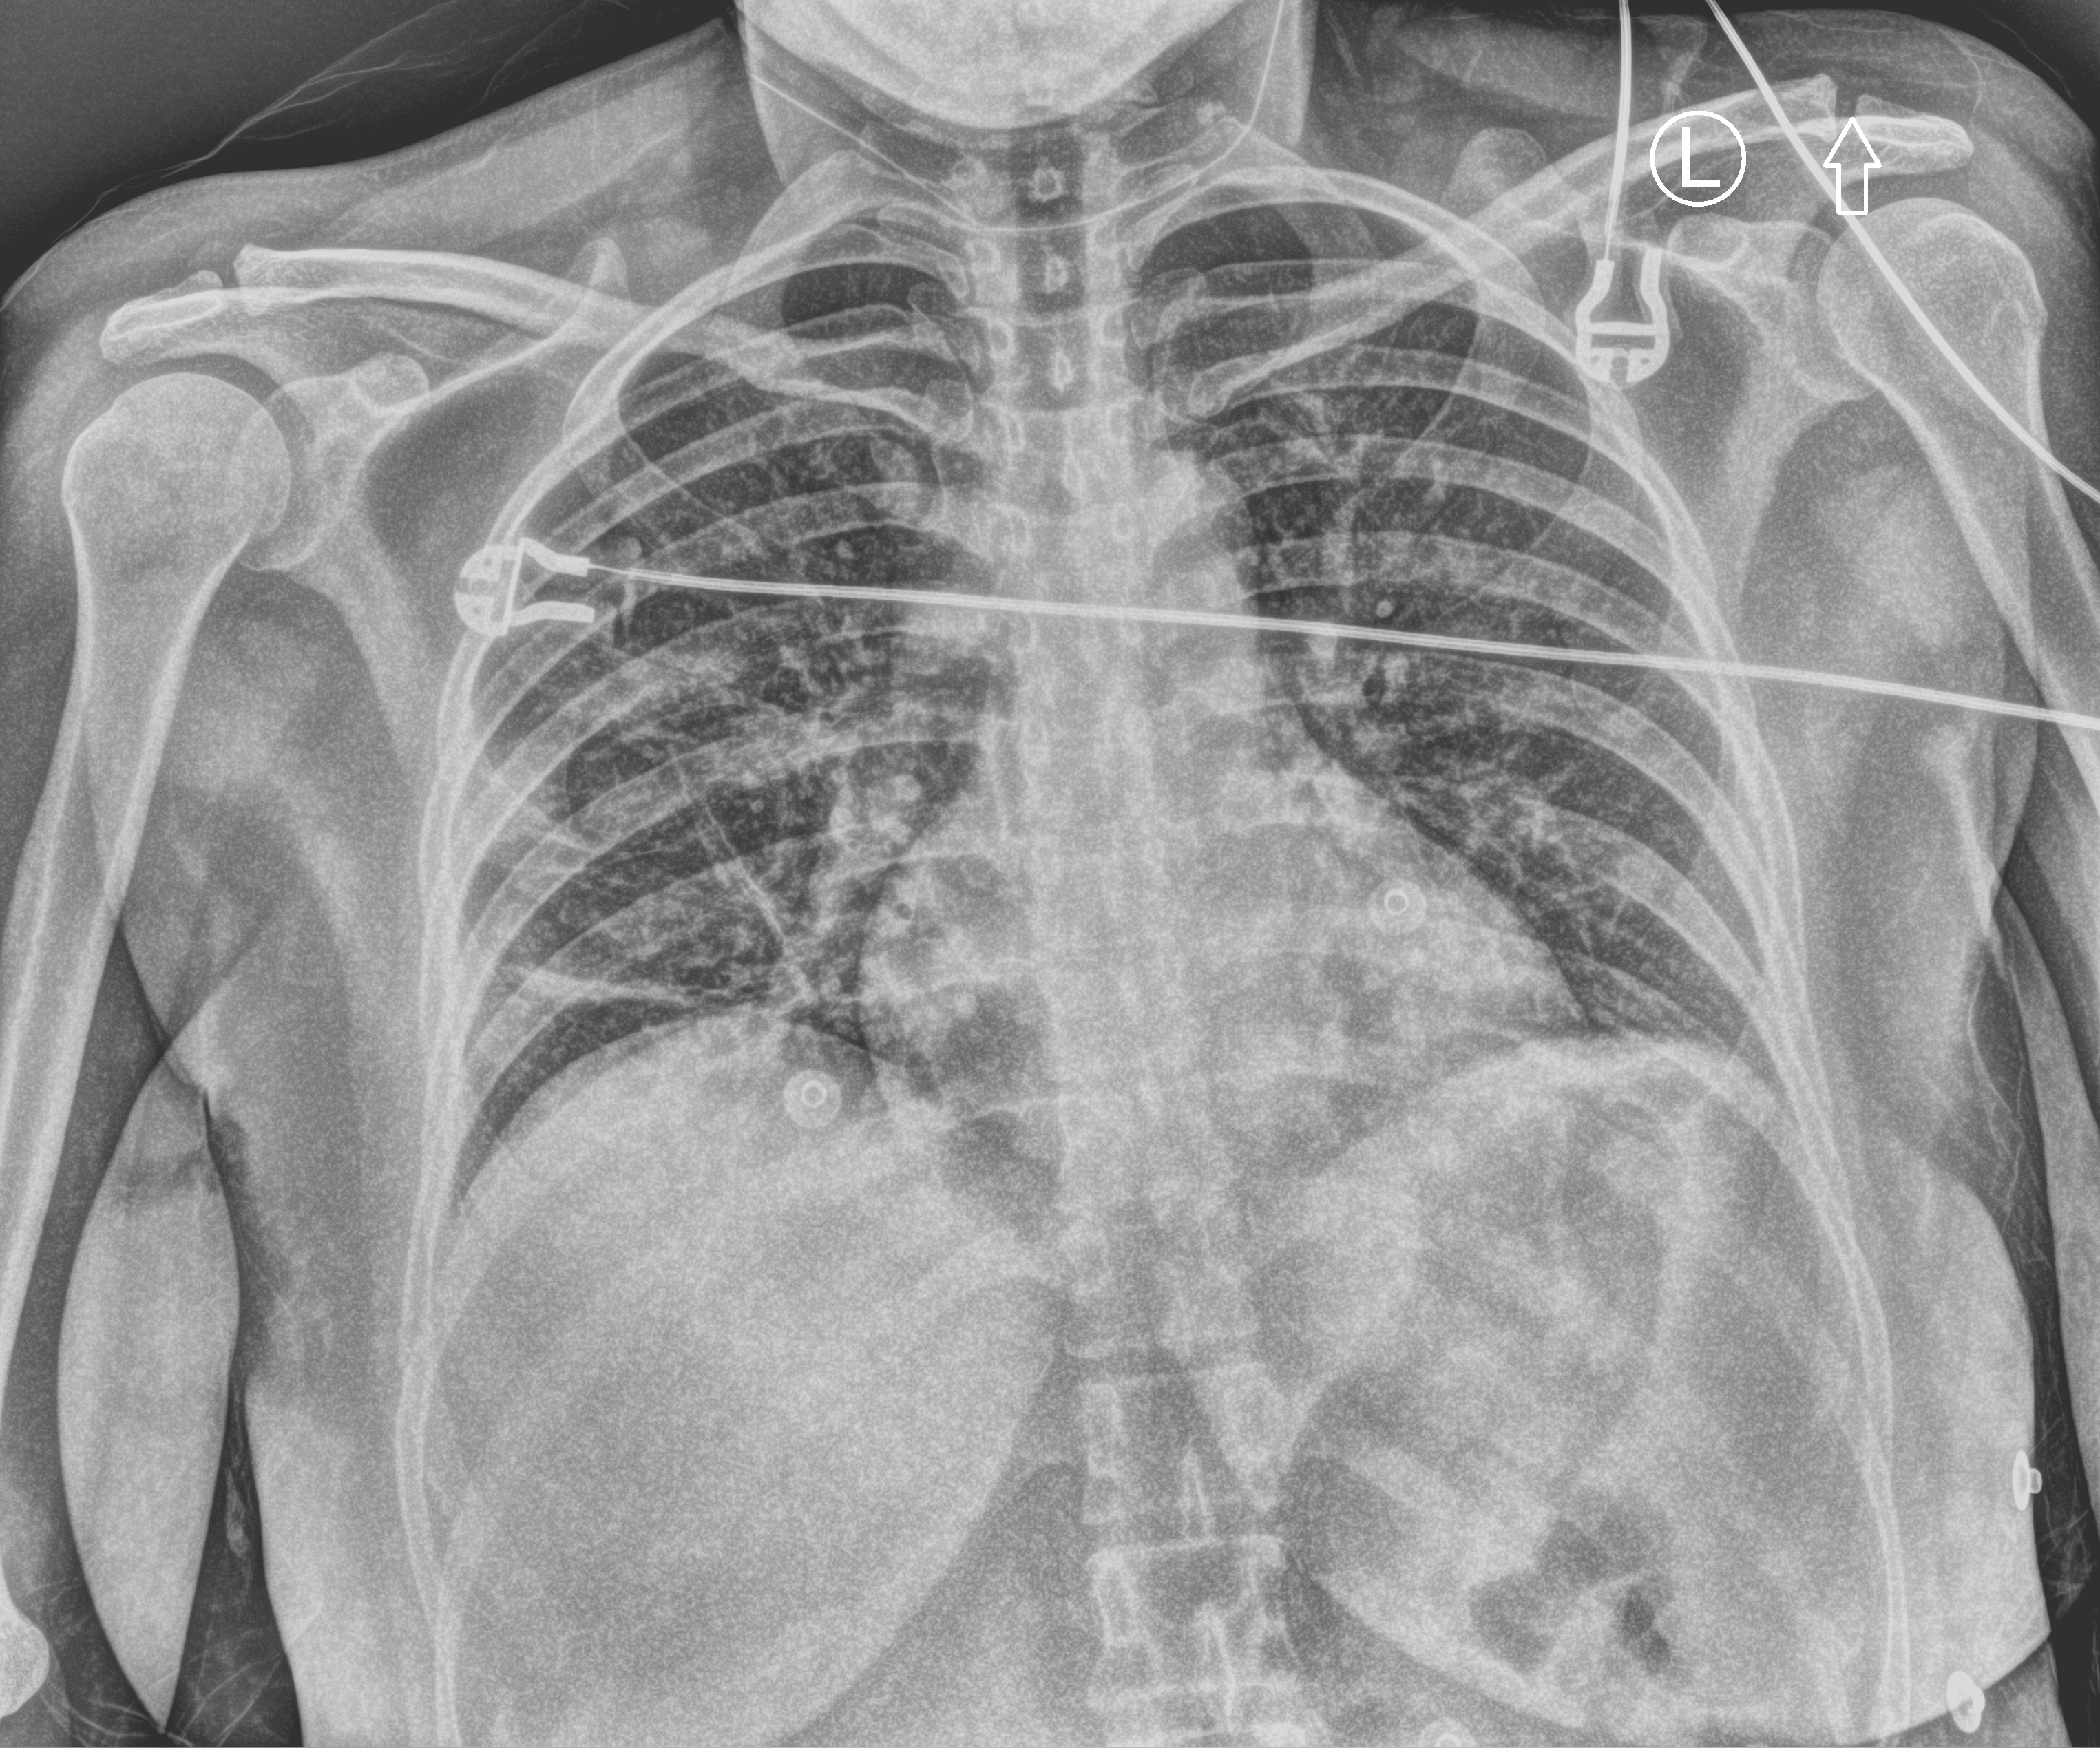
Chest X-ray (portable). Patient hospitalised with COVID-19; female, aged 18–59 years.
Admission-level facts for this patient (not findings on this image; timing relative to this image not recorded):
- hypertension (admission record): no
- mechanically ventilated during this hospital stay: no
- admitted to intensive care during this hospital stay: no